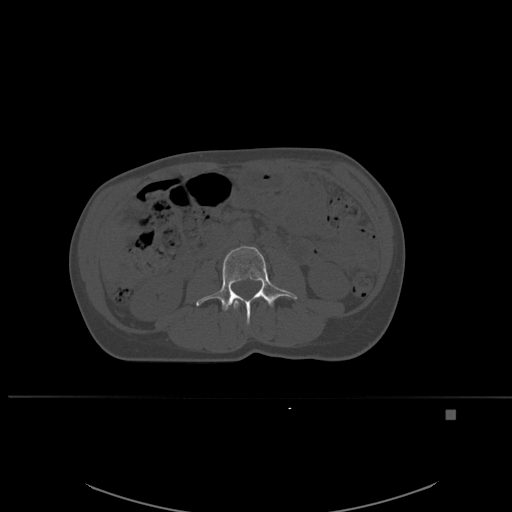
CT including the spine, one axial slice. Slice 217 of 537 in the series (ordered by position). Bone window (W 1800 / L 400 HU). 512 × 512 image matrix, field of view 440 × 440 mm. Female patient, age 45 years. Case-level facts recorded for this patient, not image findings: primary cancer: lung.
Structures marked on this image (semi-automatically segmented with operator editing):
- L2 vertebra: box from (x=233, y=298) to (x=256, y=309) px
- L3 vertebra: (x=196, y=246)–(x=298, y=325)